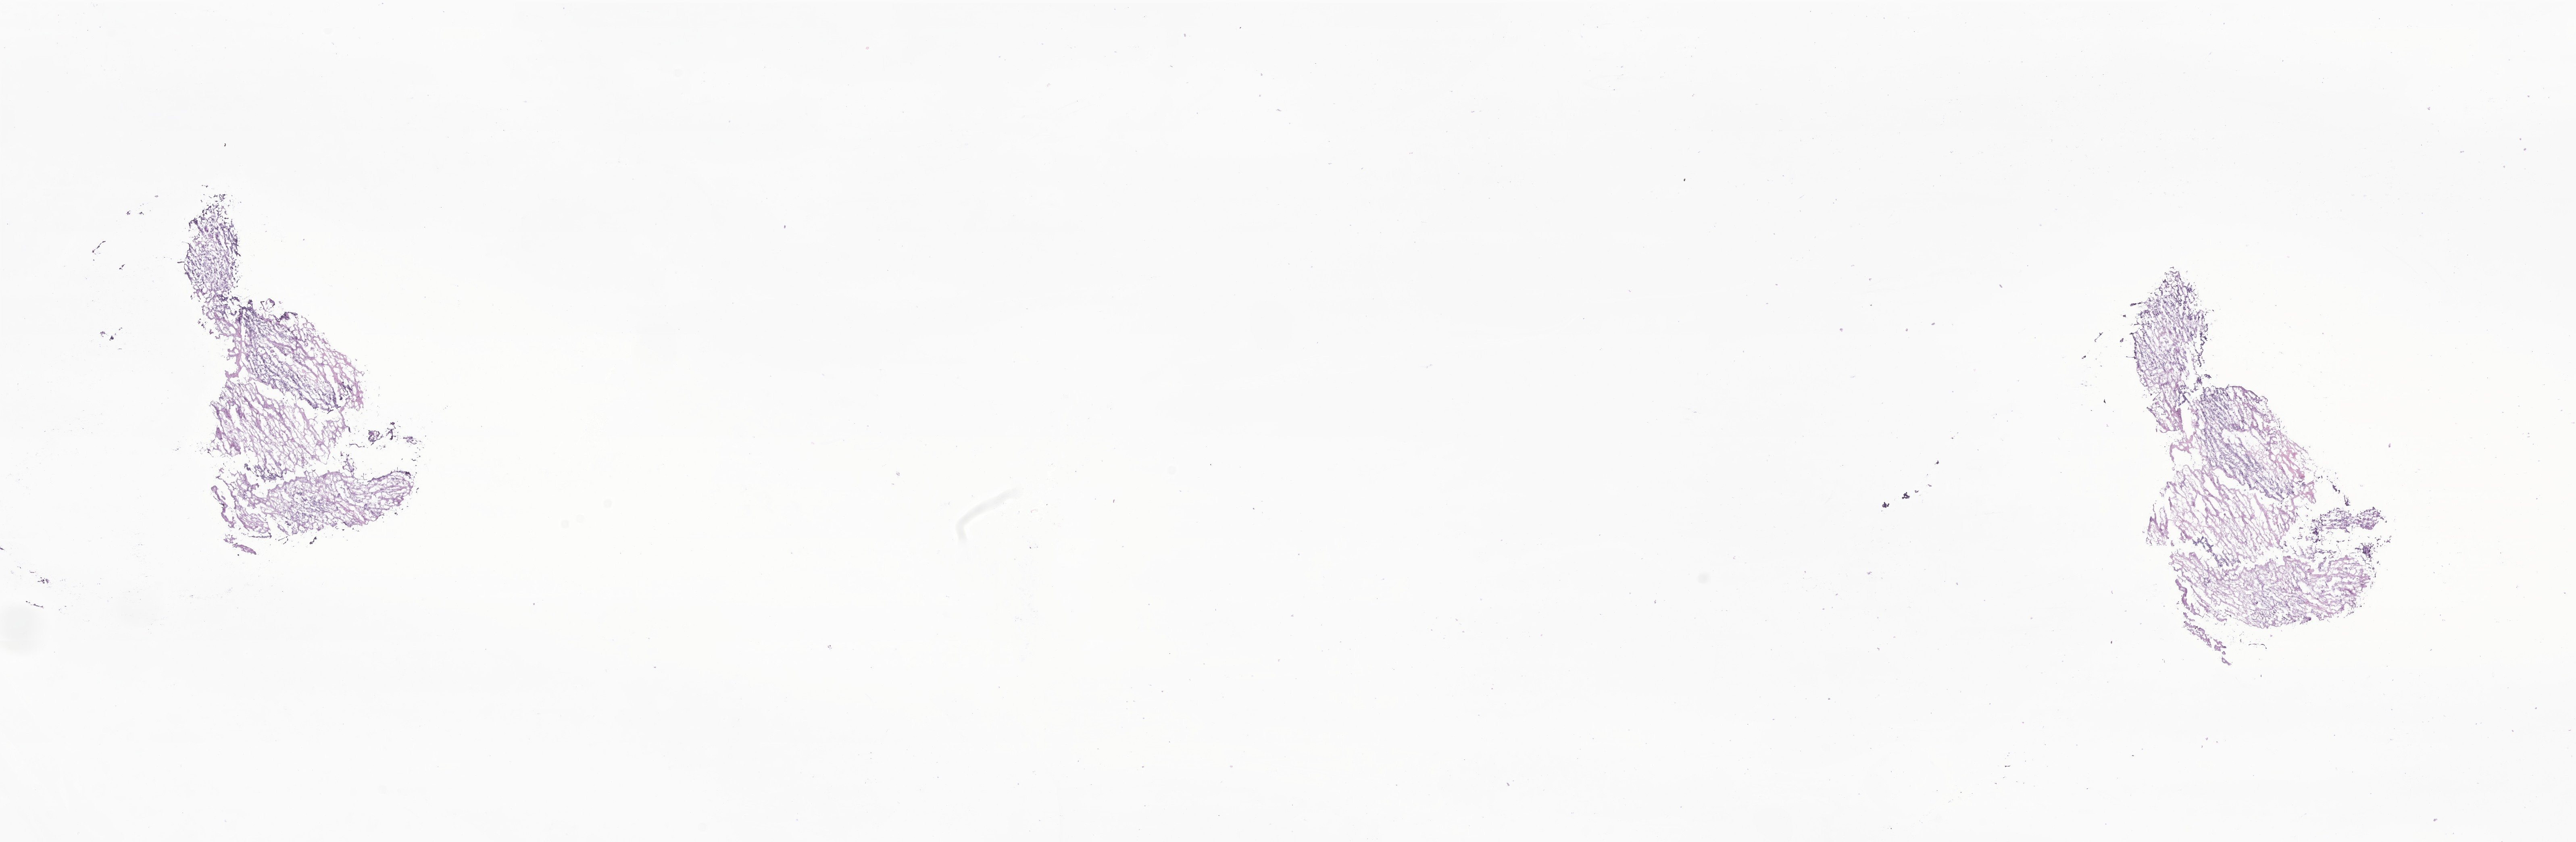
Digitized hematoxylin and eosin (H&E)-stained section of tumor tissue from the retroperitoneum, low-resolution overview of the scanned area, about 26.9 x 8.8 mm, cryosection (OCT / tissue freezing medium). Patient female; age 337 days.
Recorded diagnosis: Neuroblastoma, NOS.